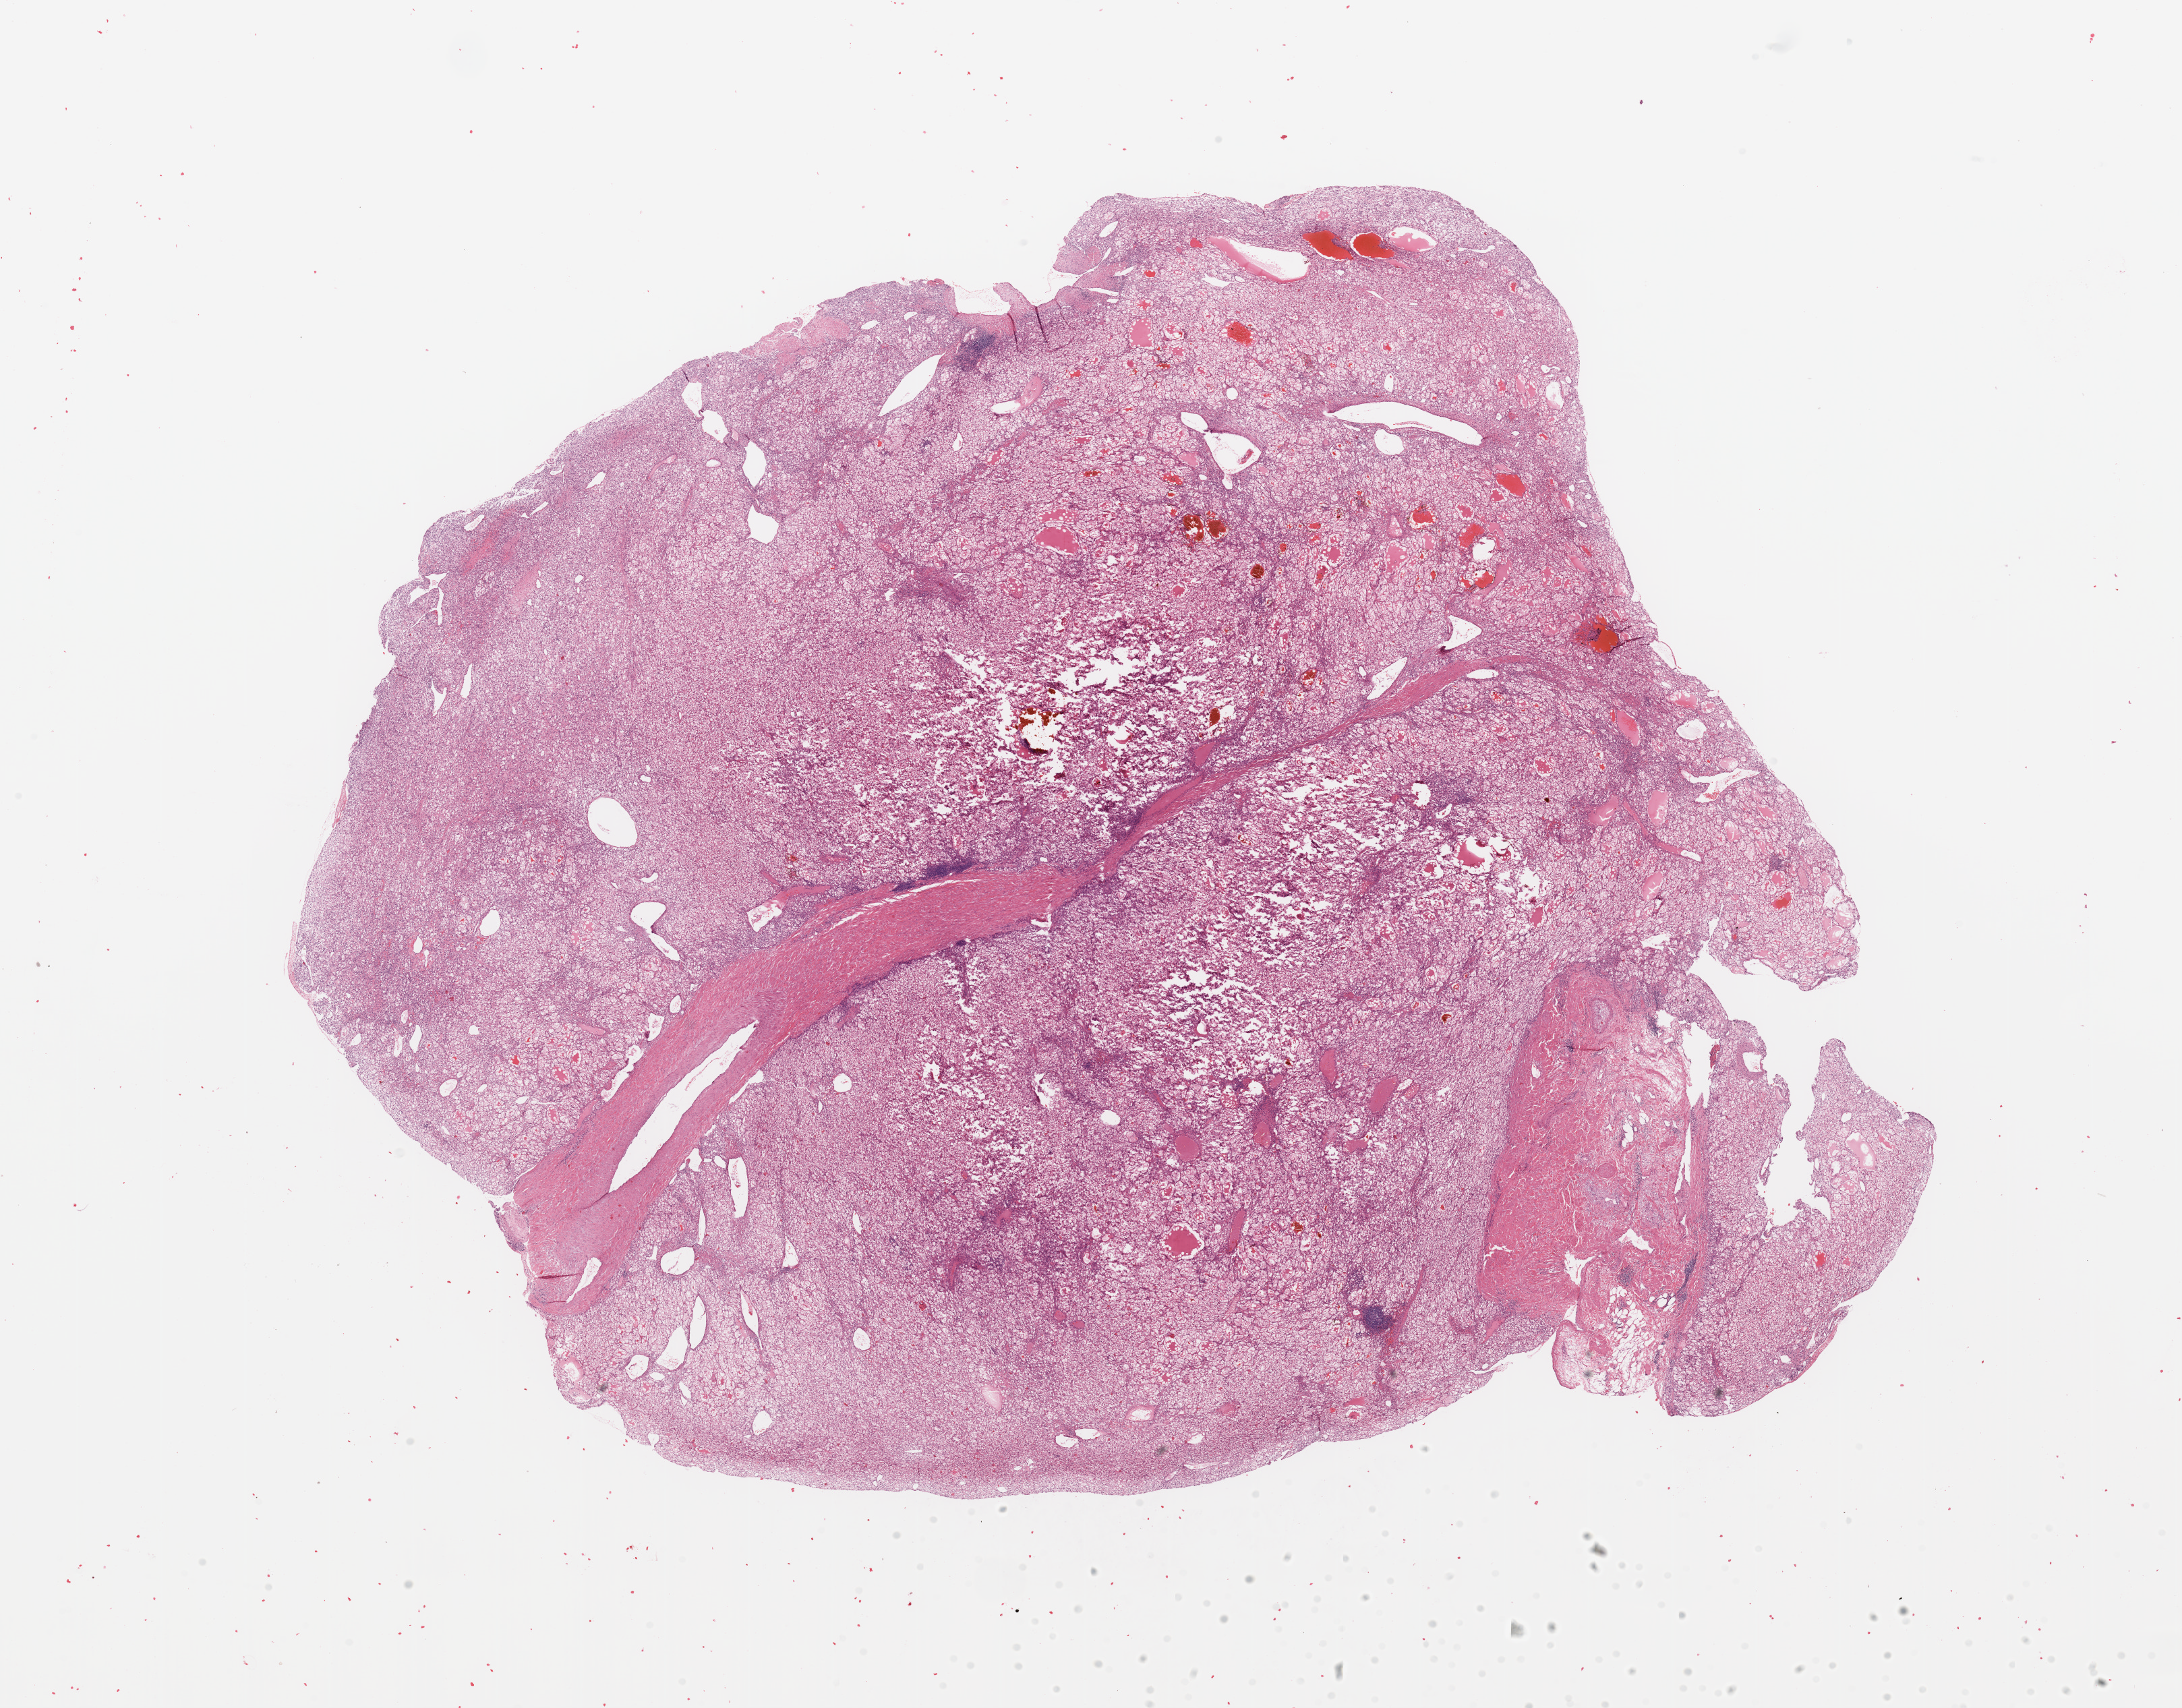
Whole-slide histology image, Hematoxylin and eosin (H&E) stained, low-resolution overview of the scanned area, about 25.6 x 20.0 mm (acquisition: 20x scan). Tumour tissue sample, kidney. Patient: female, age 42 years. Histologic grade: G2 (moderately differentiated).
Histologic diagnosis: Renal cell carcinoma, NOS.